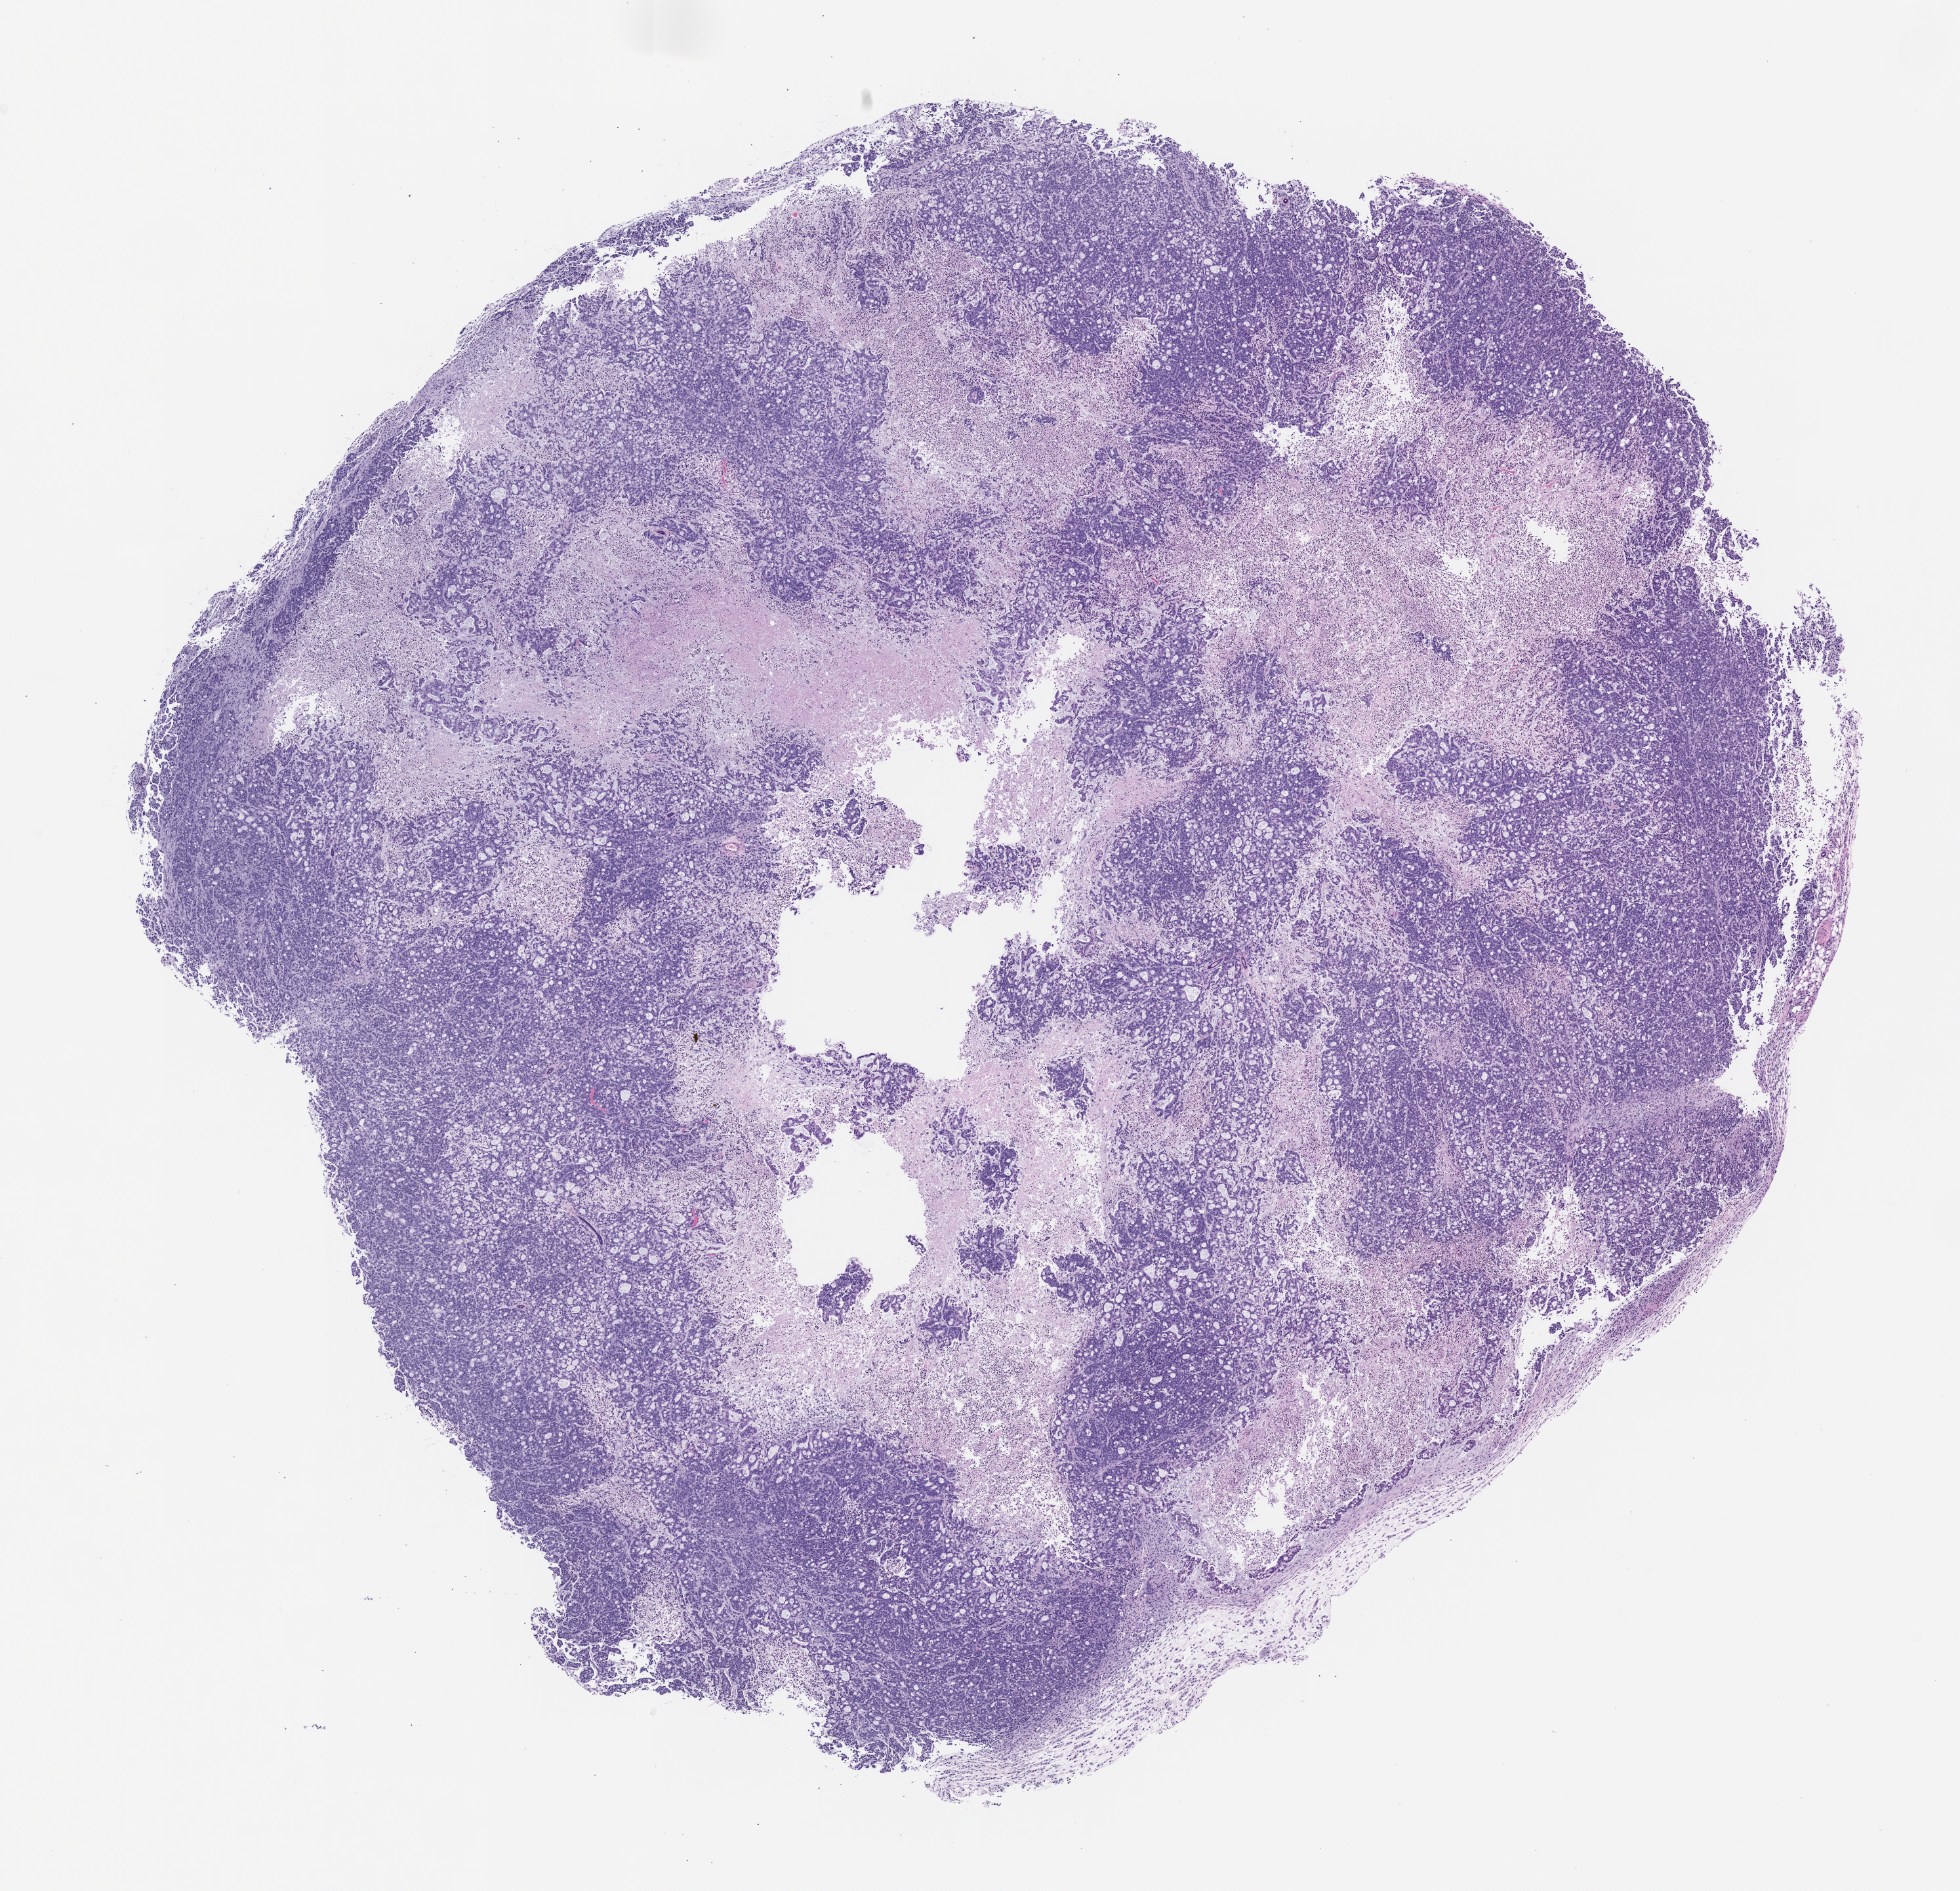
Whole-slide image, haematoxylin and eosin: patient-derived xenograft (human tumor grown in a mouse), passage 1 — shown as a low-resolution overview of the whole scanned area (about 12.0 x 11.6 mm); FFPE section; originating tumor site category: colon.
Originating patient diagnosis: Colon Adenocarcinoma.